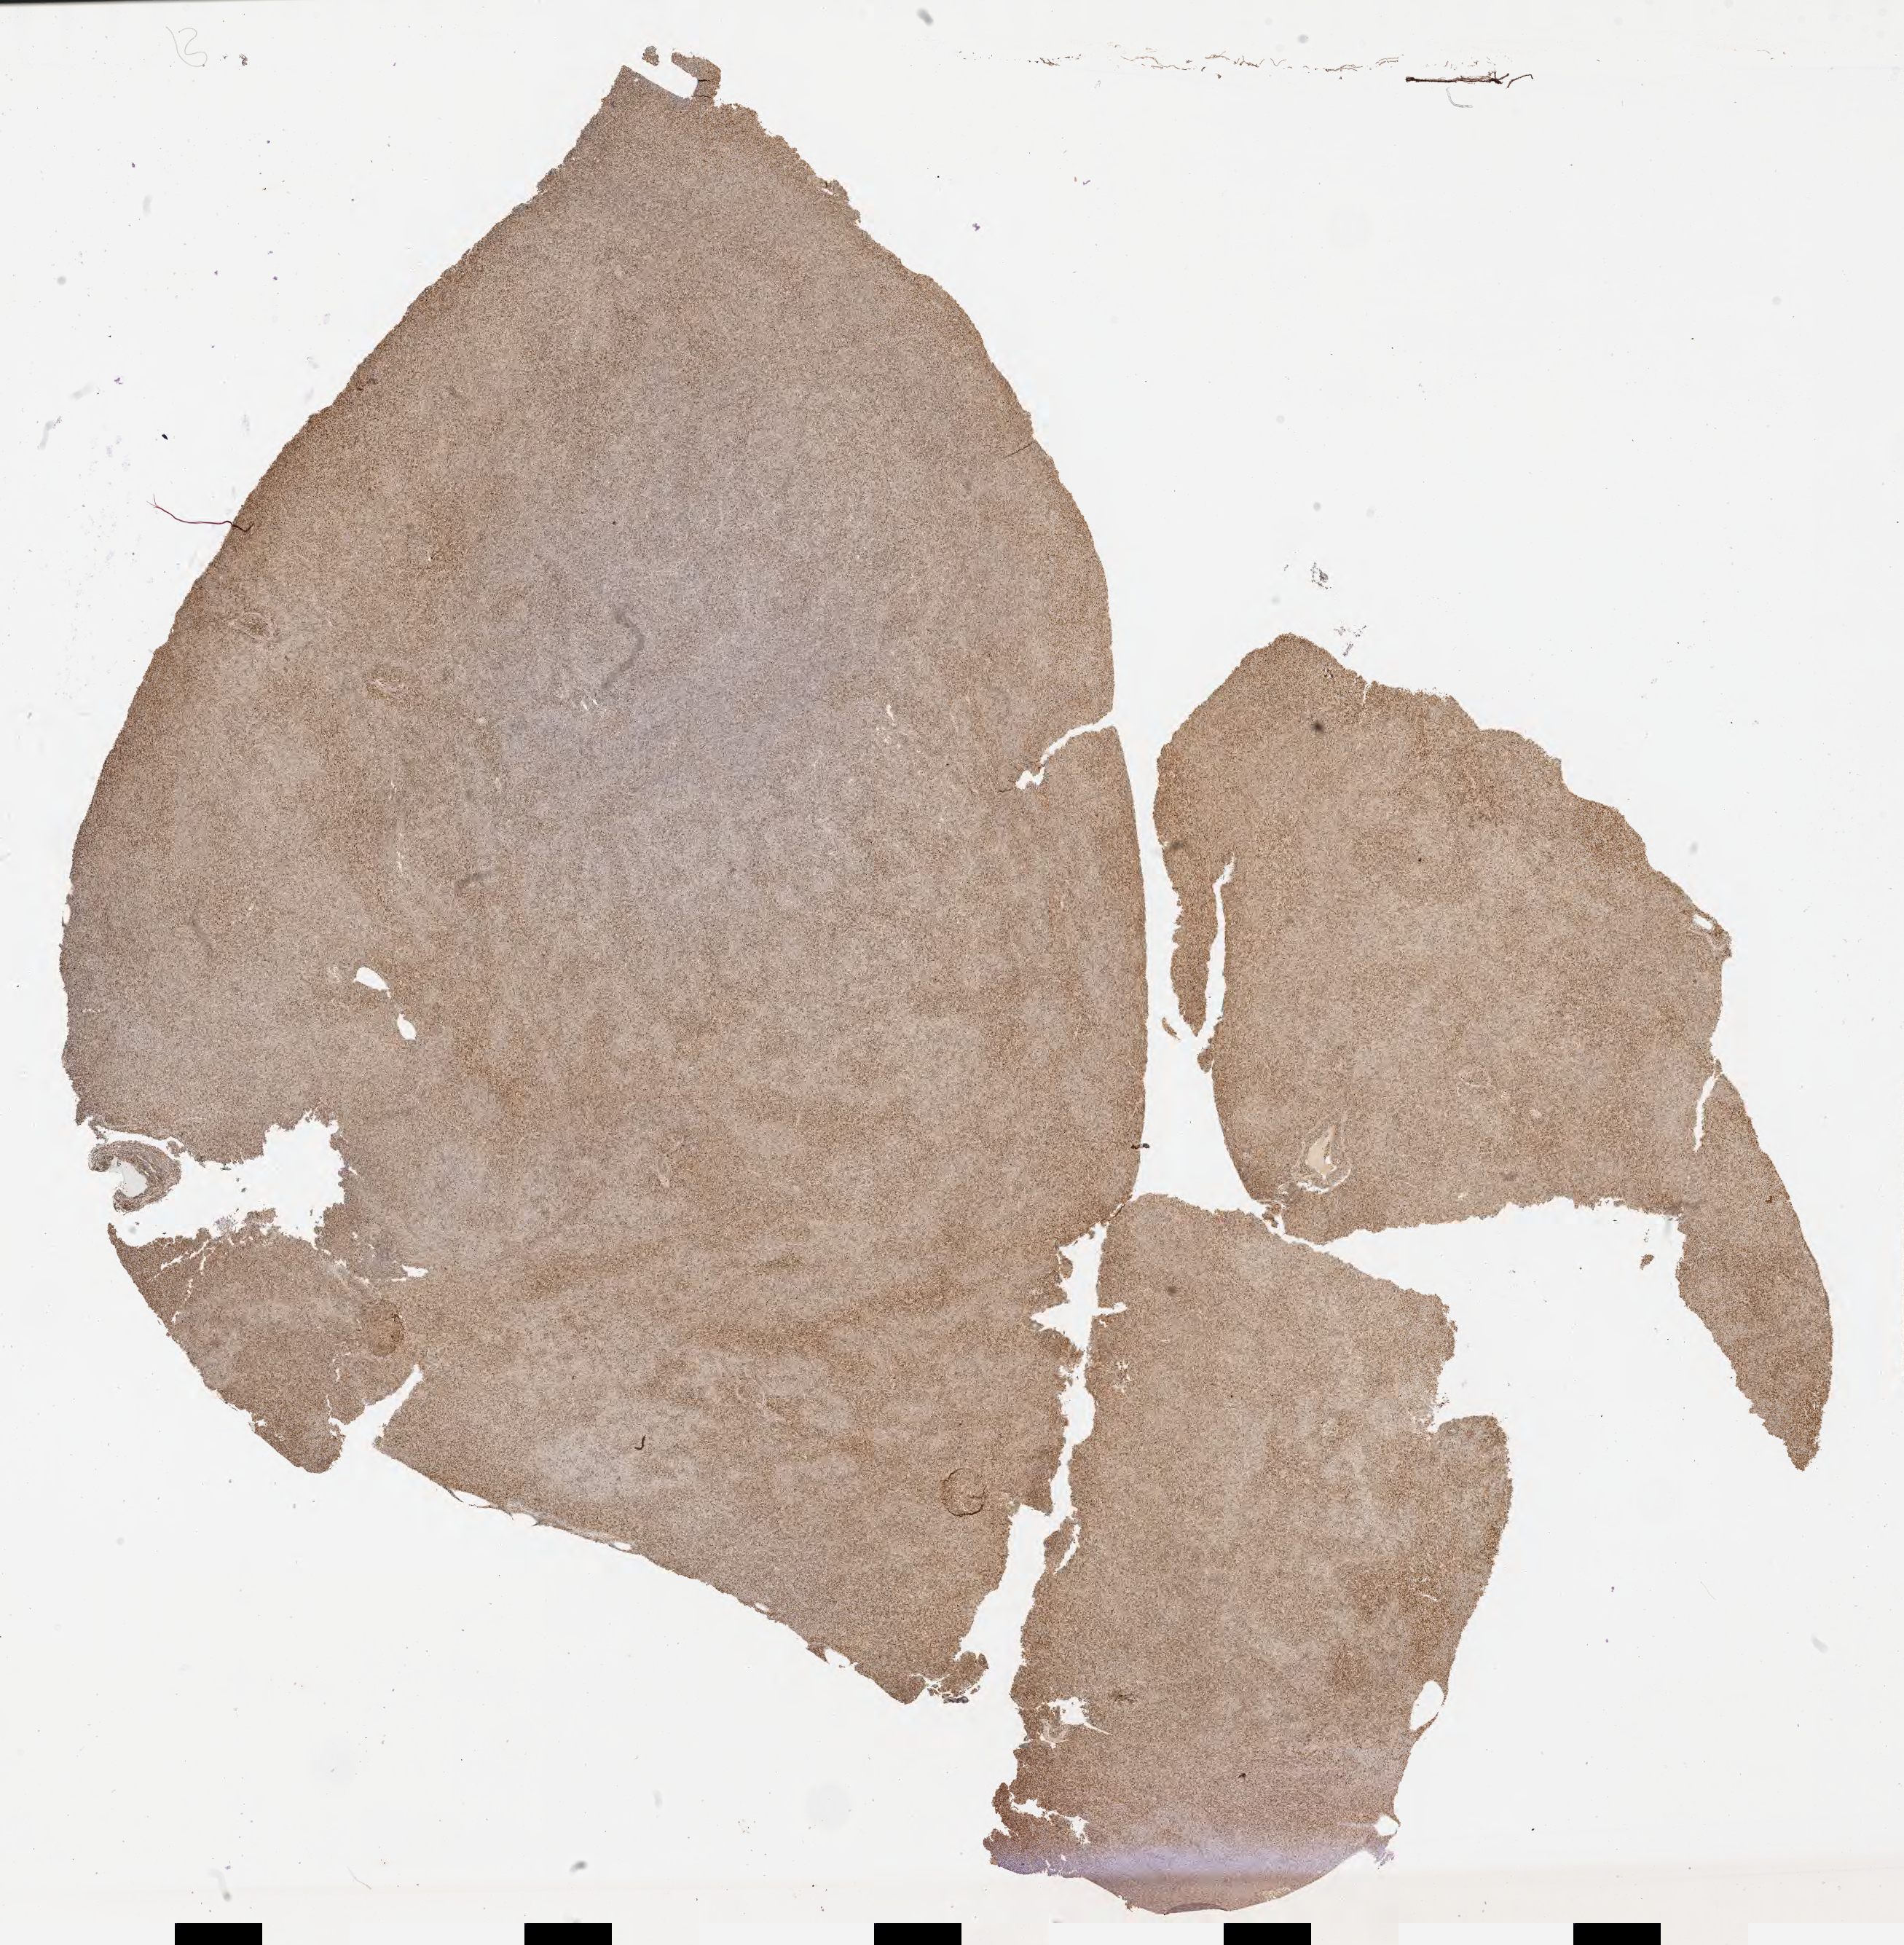
Whole-slide image, immunohistochemical stain for BCL2, shown as a low-resolution overview of the whole scanned area (about 21.1 x 21.6 mm), specimen: tumor tissue, anatomic site: liver. Patient female; age 46 years.
Diagnosis: Diffuse large B-cell lymphoma, NOS.